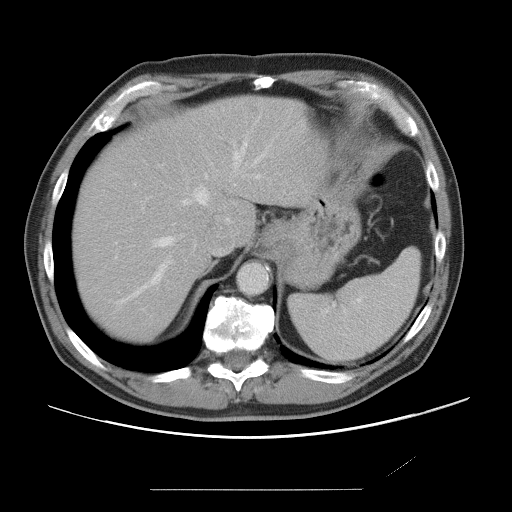
Contrast-enhanced abdominal CT, one axial slice. Slice 58 of 87 in the series (ordered by position). Intravenous contrast given. Soft-tissue window (W 400 / L 40 HU). 5 mm slice thickness. 512 × 512 image matrix, field of view 406 × 406 mm. Male patient, age 74 years. Case-level facts recorded for this patient, not image findings: diagnosis: colorectal cancer liver metastases, imaged before liver resection; multiple liver metastases: yes; largest metastasis: 1.1 cm; disease in both lobes: no.
Outlined on this slice (outlined manually by an expert reader):
- hepatic veins: bounding box [x1, y1, x2, y2] px = [119, 143, 265, 303]
- liver: [74, 96, 312, 343]
- planned liver remnant (the part of the liver to remain after resection): [74, 97, 311, 343]
- portal vein (with intrahepatic branches): [116, 174, 208, 258]